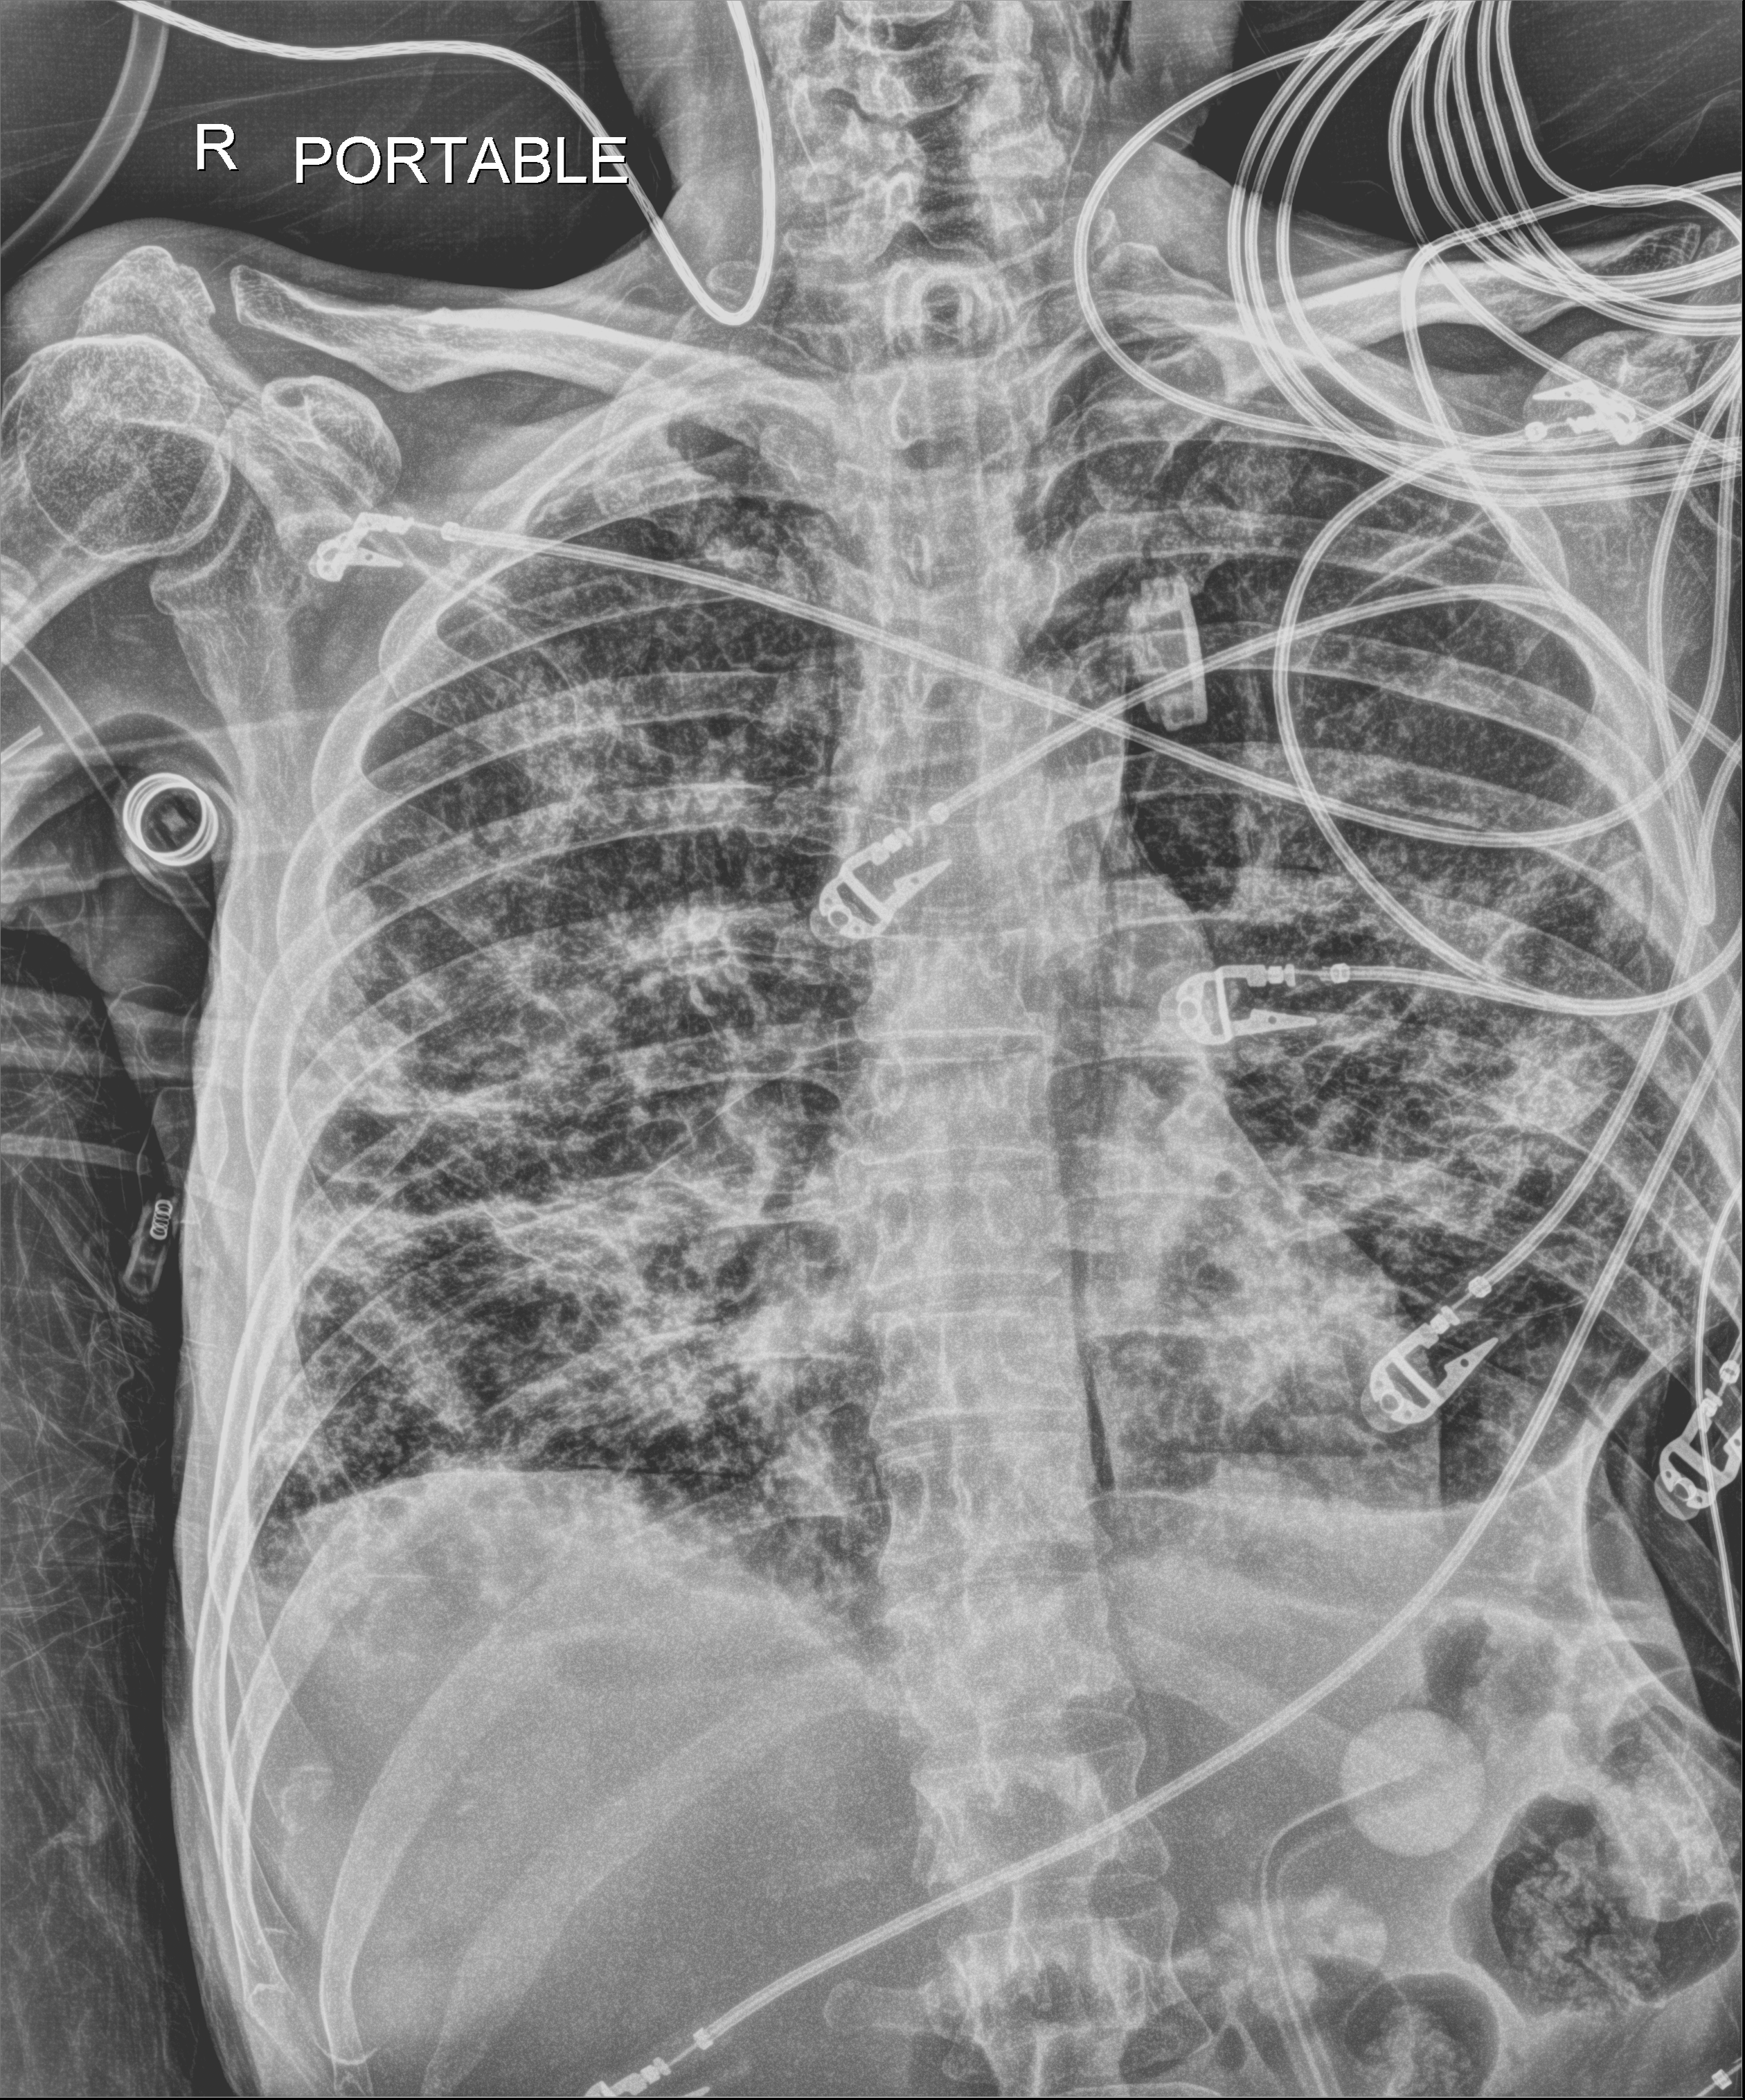
Chest radiograph, anteroposterior (AP) projection. Patient hospitalised with COVID-19; male, aged 18–59 years.
From the hospital-stay record, not from the radiograph (when in the stay this image was taken is not recorded): admitted to intensive care during this hospital stay: yes.